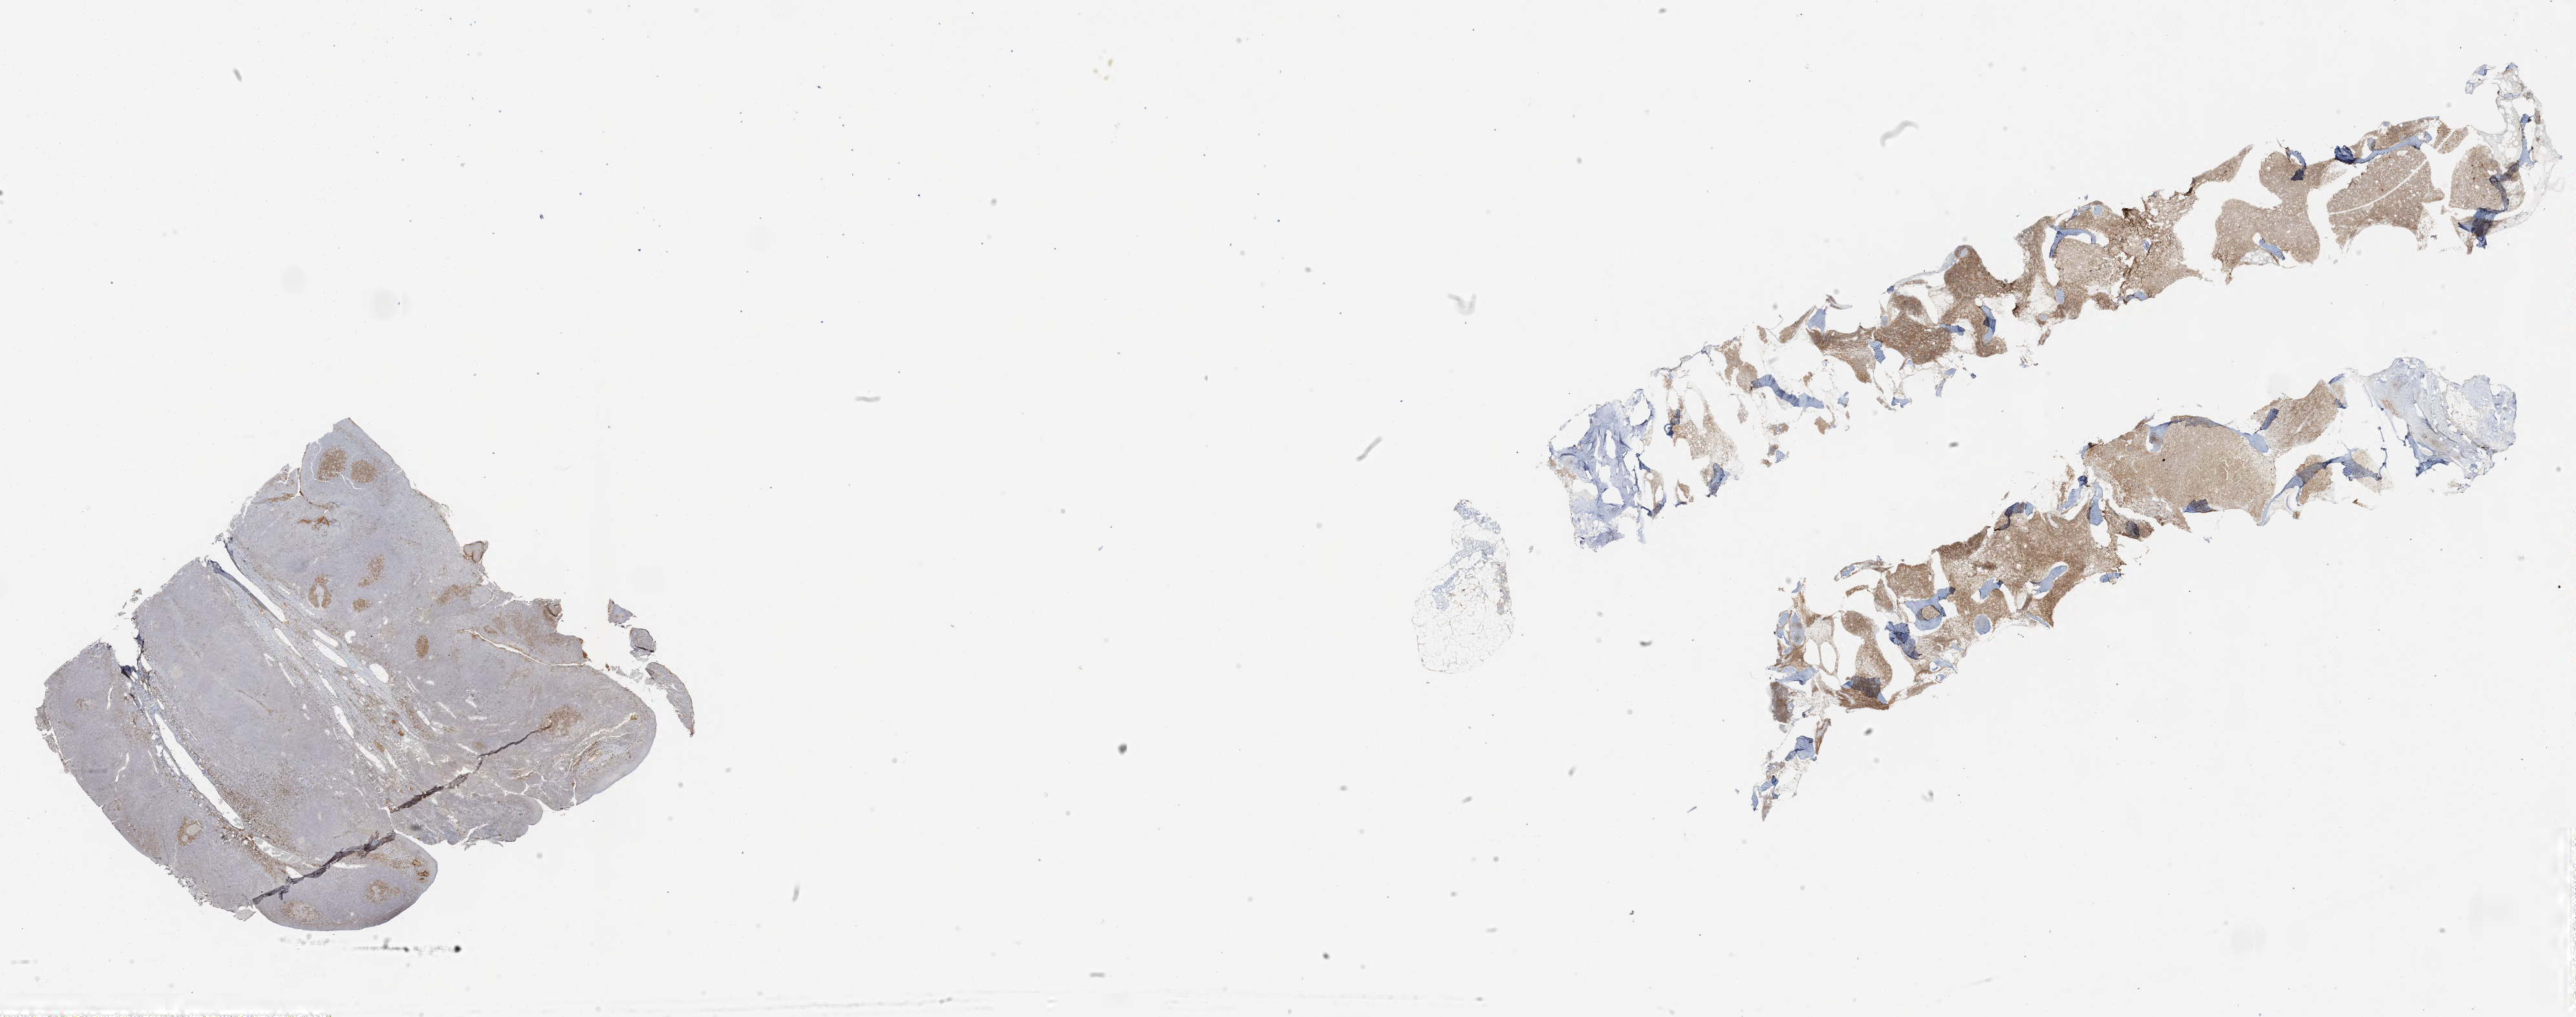
IHC for CD10, whole-slide image, low-resolution overview of the scanned area, about 32.0 x 12.6 mm. Tumor tissue. Patient female; 60 years old.
Histologic diagnosis: Burkitt lymphoma, NOS.